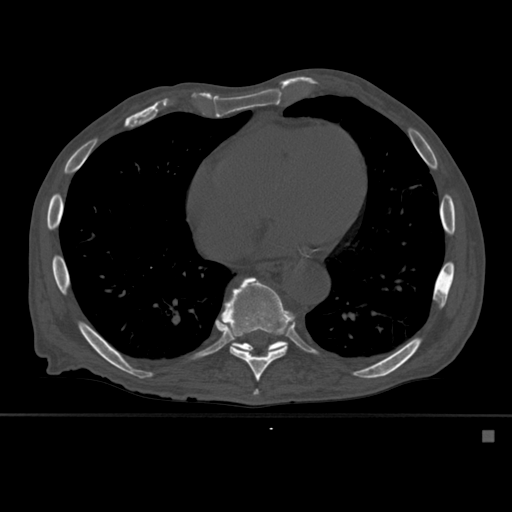
CT including the spine, one axial slice; position 329 of 527 along the scan axis; bone window (W 1800 / L 400 HU); 512 × 512 image matrix. Male patient, age 78 years. Case-level facts recorded for this patient, not image findings: primary cancer: prostate.
Outlined on this slice (semi-automatic segmentation, software-assisted and operator-edited):
- T10 vertebra: bounding box [x1, y1, x2, y2] px = [231, 341, 285, 353]
- T8 vertebra: [253, 389, 259, 395]
- T9 vertebra: [221, 277, 295, 381]